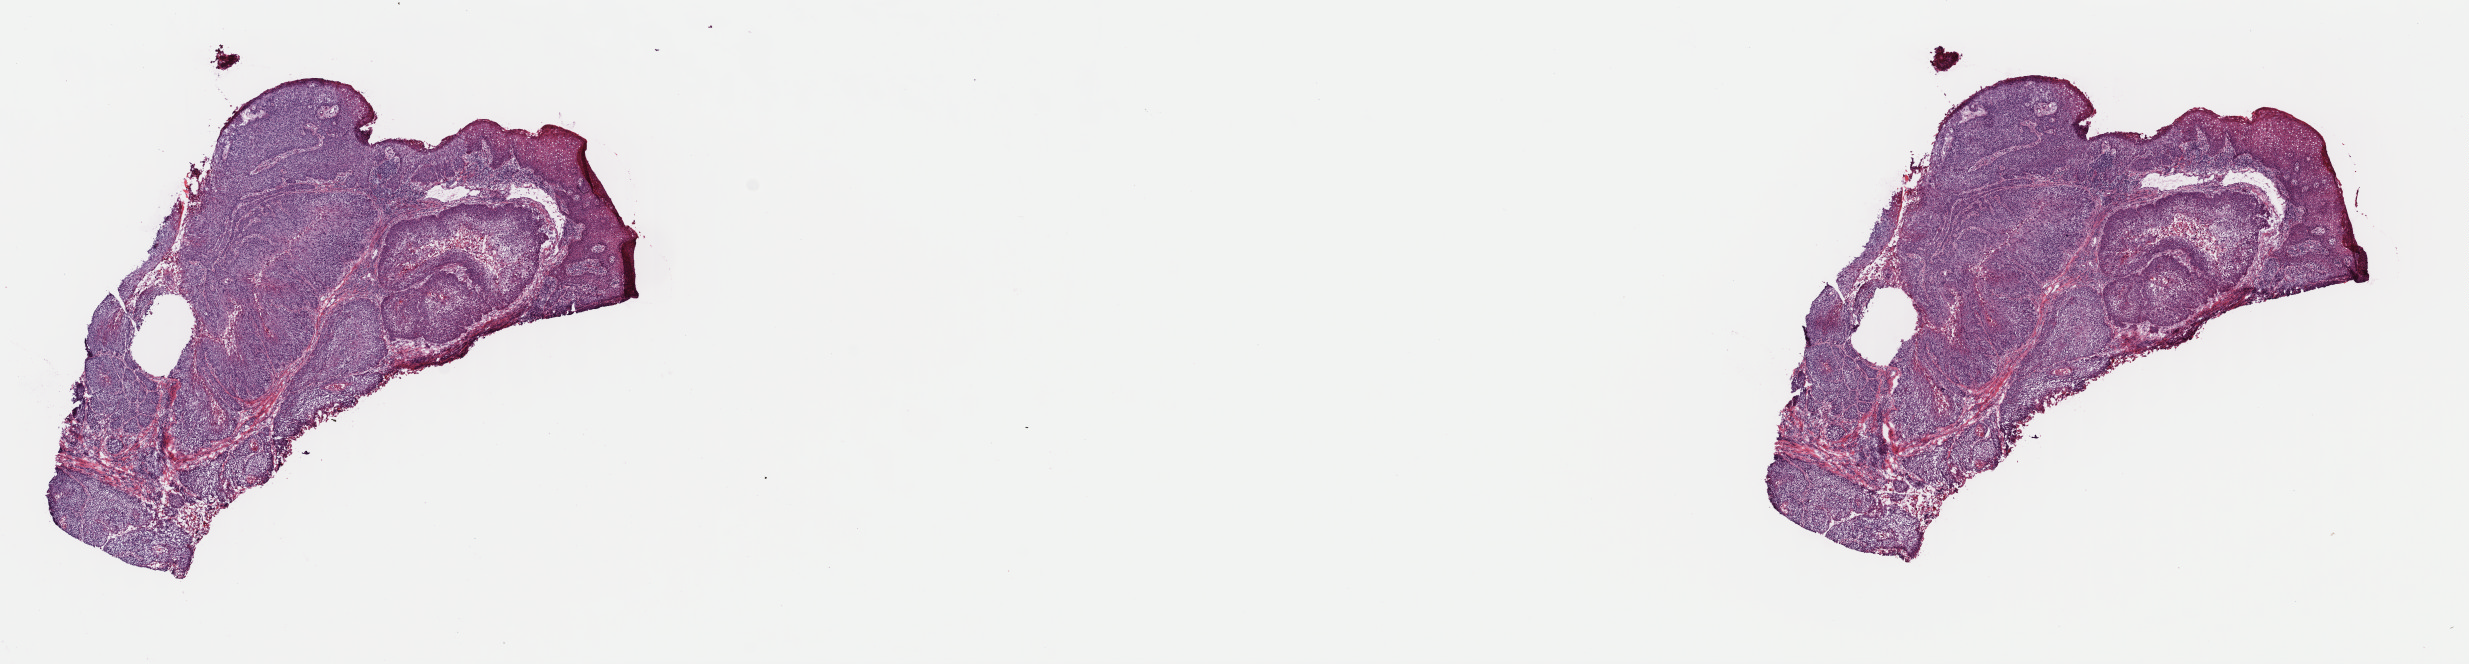
Digitized H&E-stained tissue section (whole slide) — whole scanned area (about 19.5 x 5.2 mm, slide scanned at 40x) shown as a low-resolution overview. Frozen section. Primary tumour sample from the head and neck. Female patient; age at initial diagnosis 54 years. Composition of this section per pathologist review: tumour cells 80%, tumour nuclei 90%.
Diagnosis: Squamous cell carcinoma, NOS (larynx, NOS).